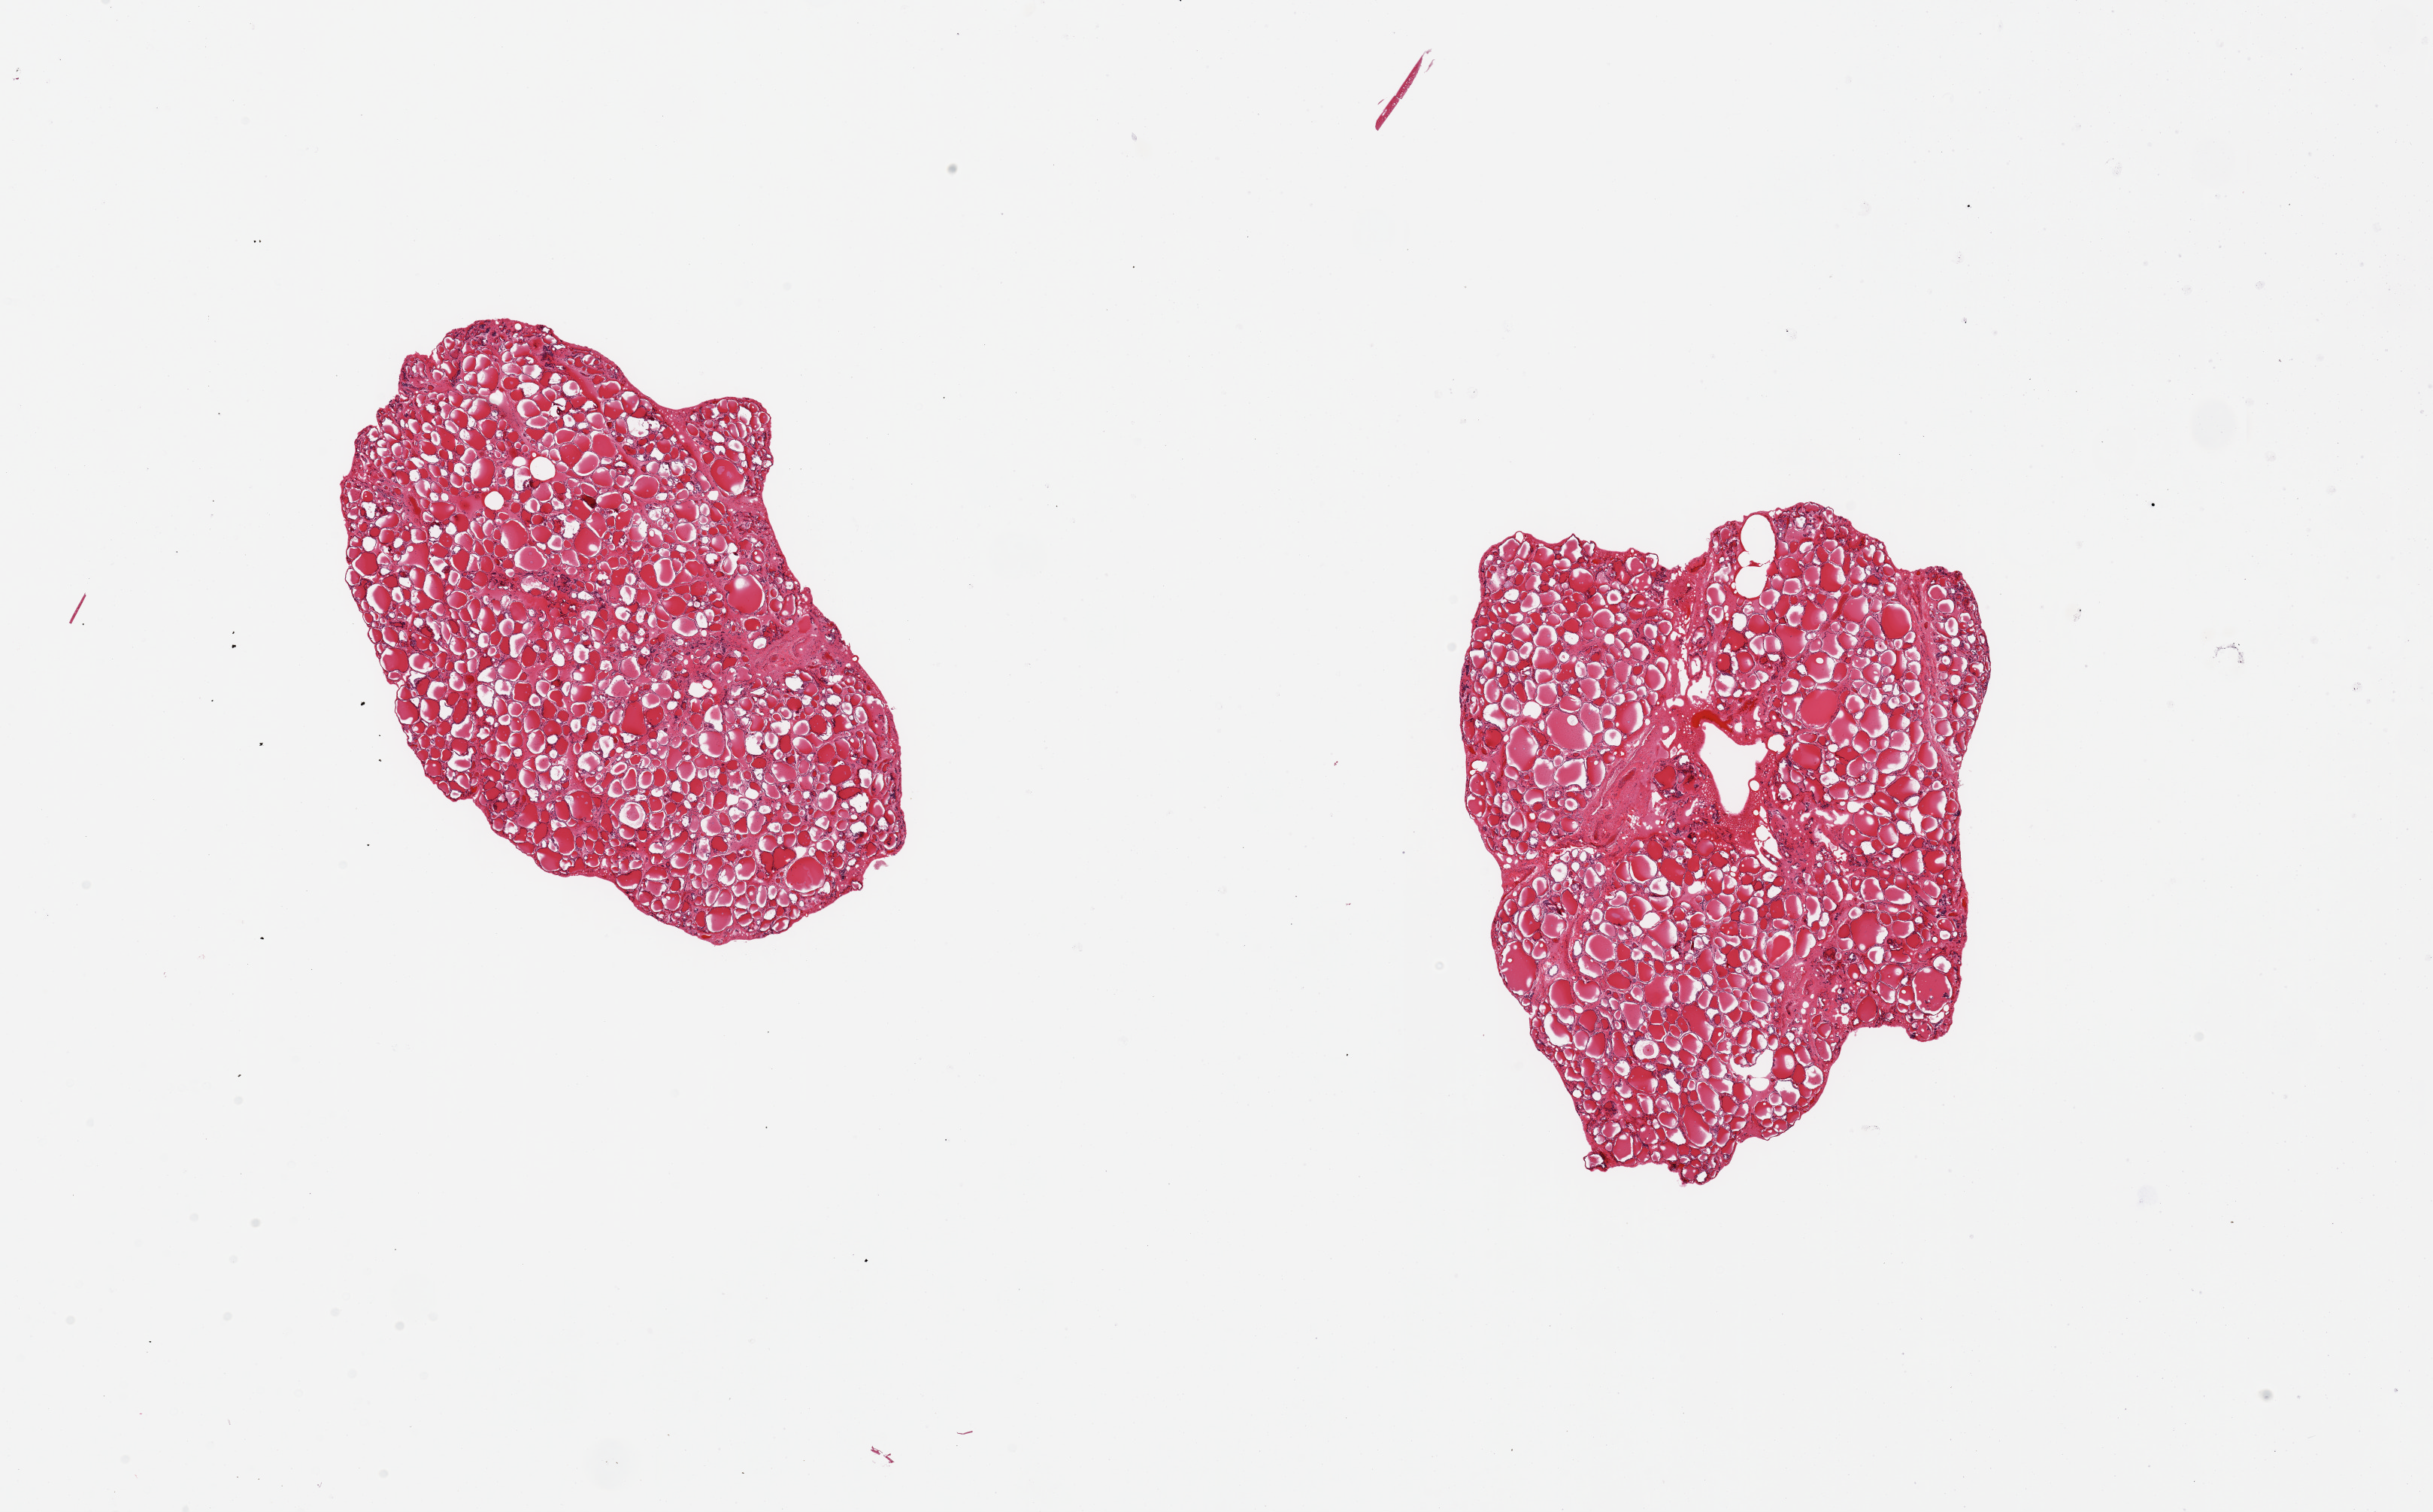
H&E whole-slide image — a low-resolution overview of the entire scanned area, about 25.6 x 15.9 mm, PAXgene-fixed, paraffin-embedded tissue, section of thyroid (target tissue), tissue donor sample.
- reviewer comment on this tissue sample: 2 pieces